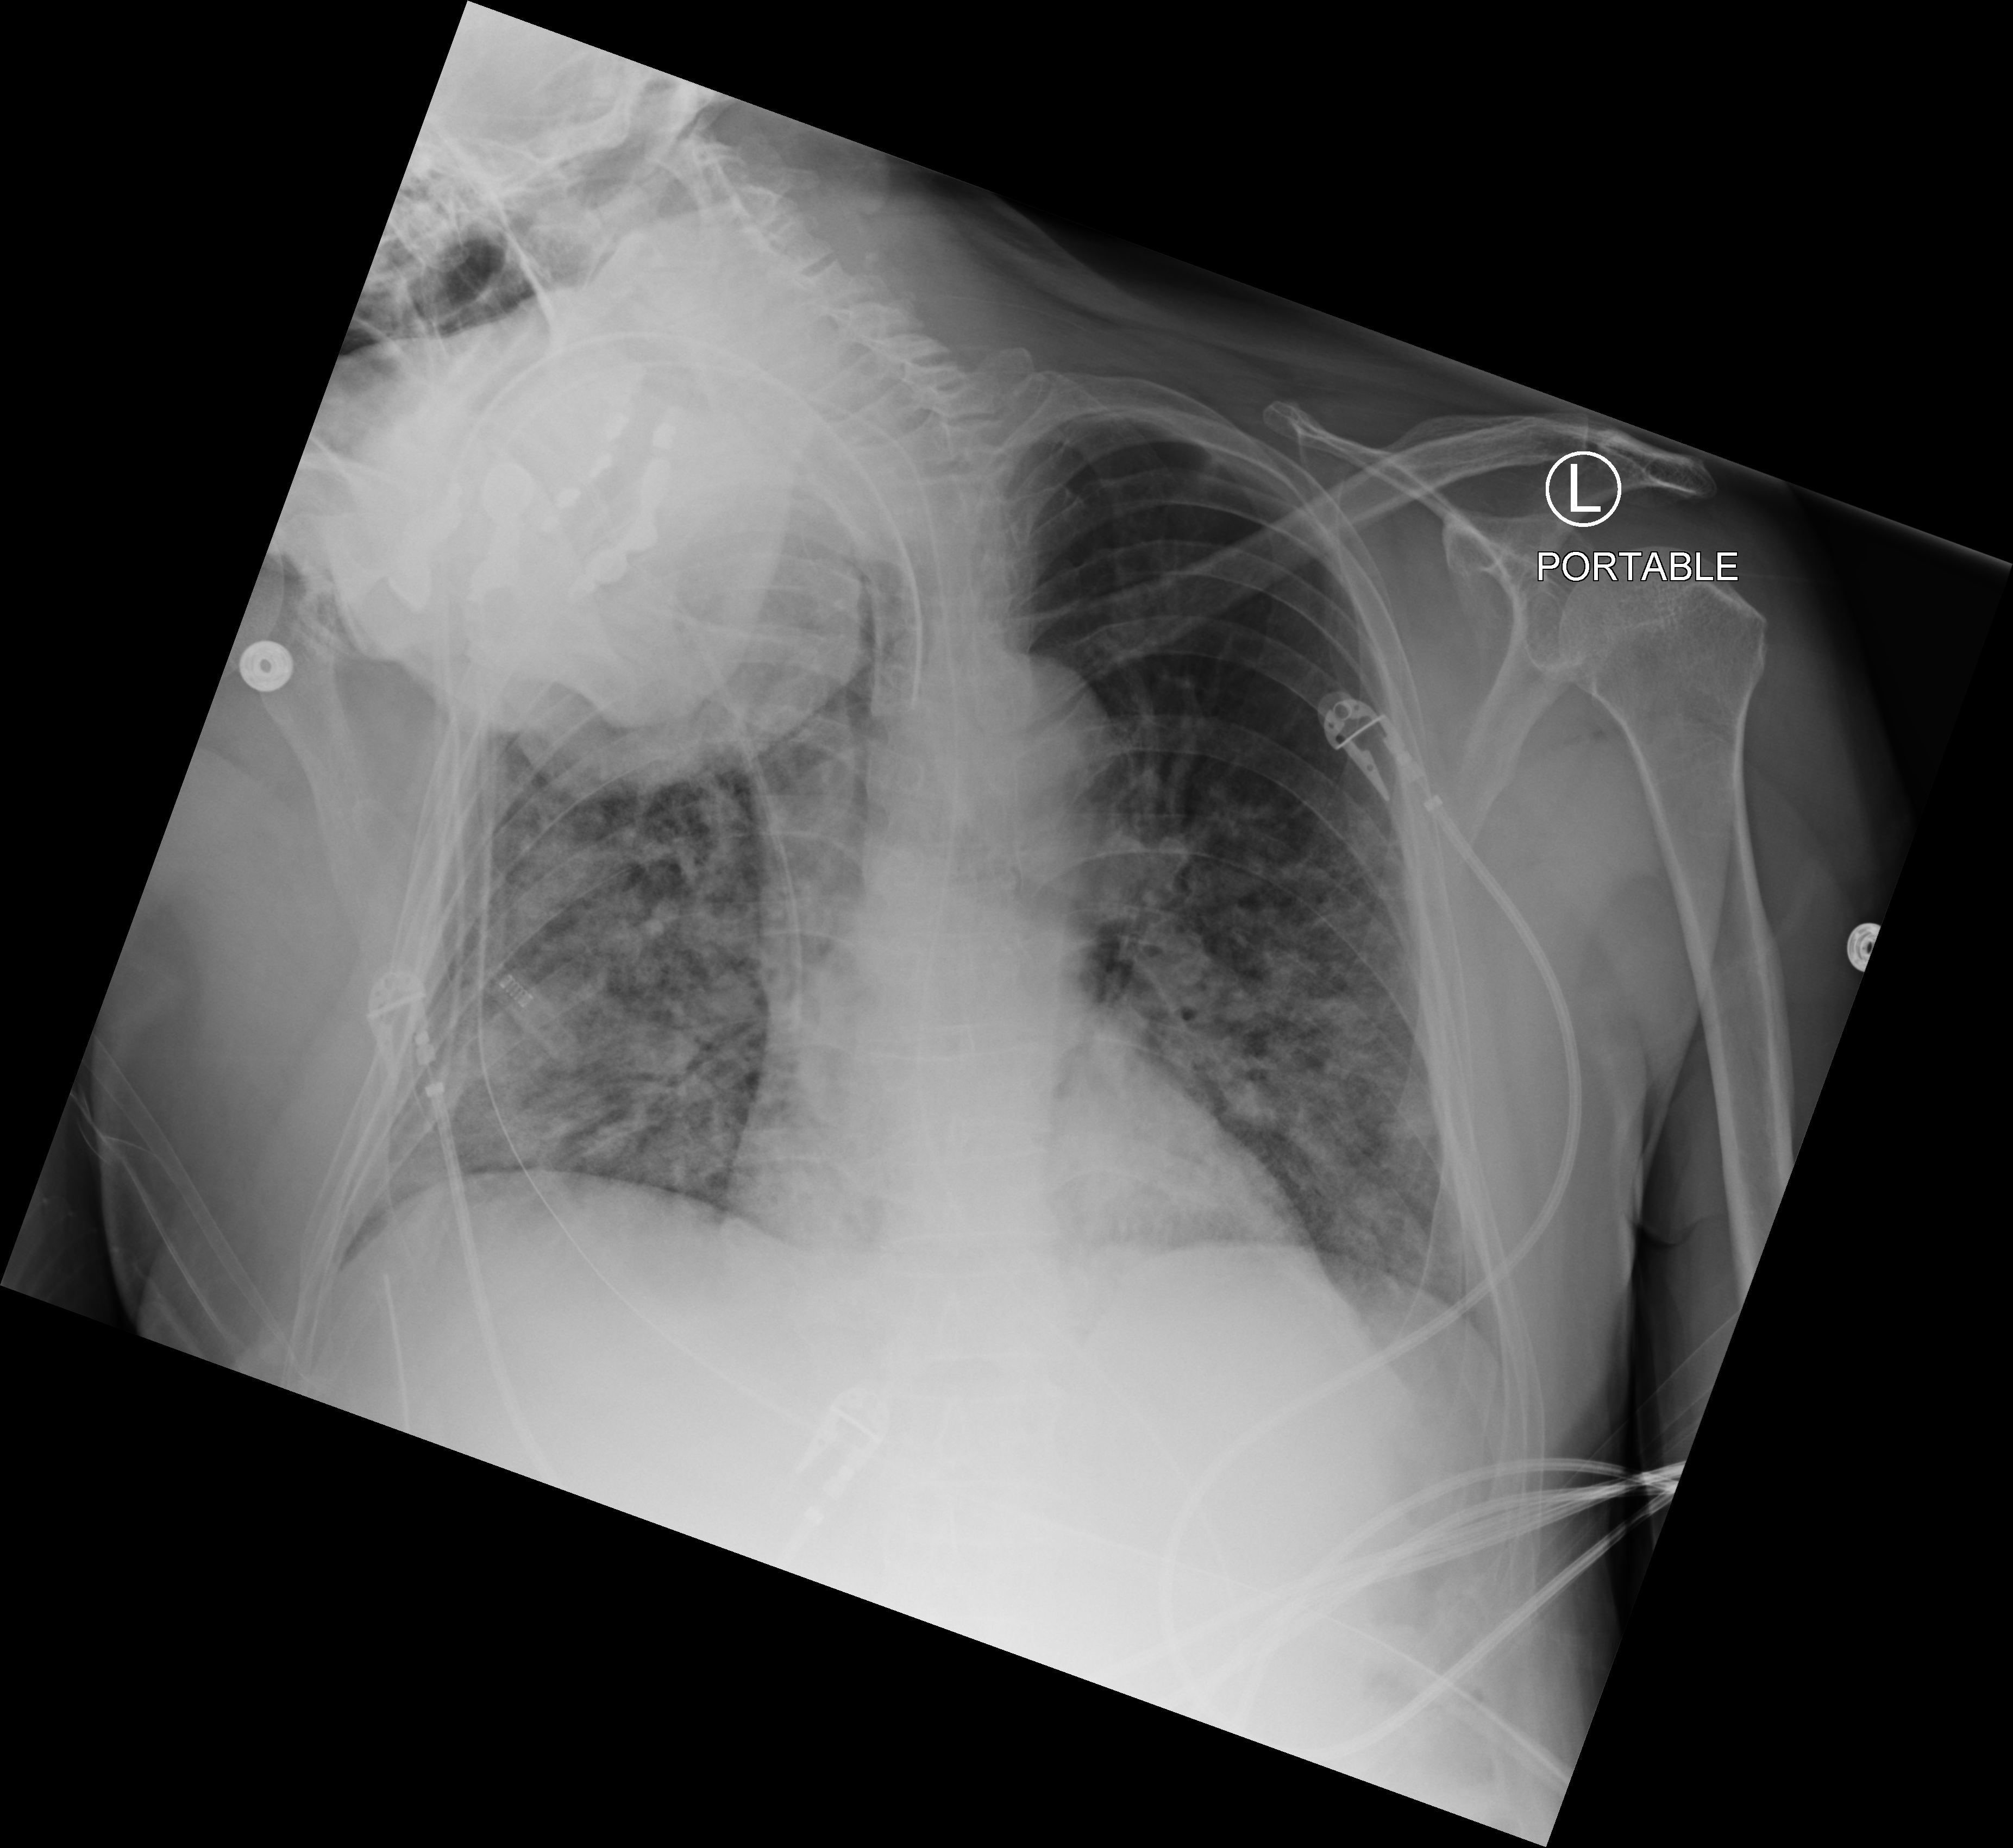
Chest X-ray (portable), anteroposterior (AP) projection. Patient hospitalised with COVID-19; male, aged 60–74 years.
From the hospital-stay record, not from the radiograph (when in the stay this image was taken is not recorded):
- length of hospital stay: 19 days
- admitted to intensive care during this hospital stay: yes
- mechanically ventilated during this hospital stay: yes